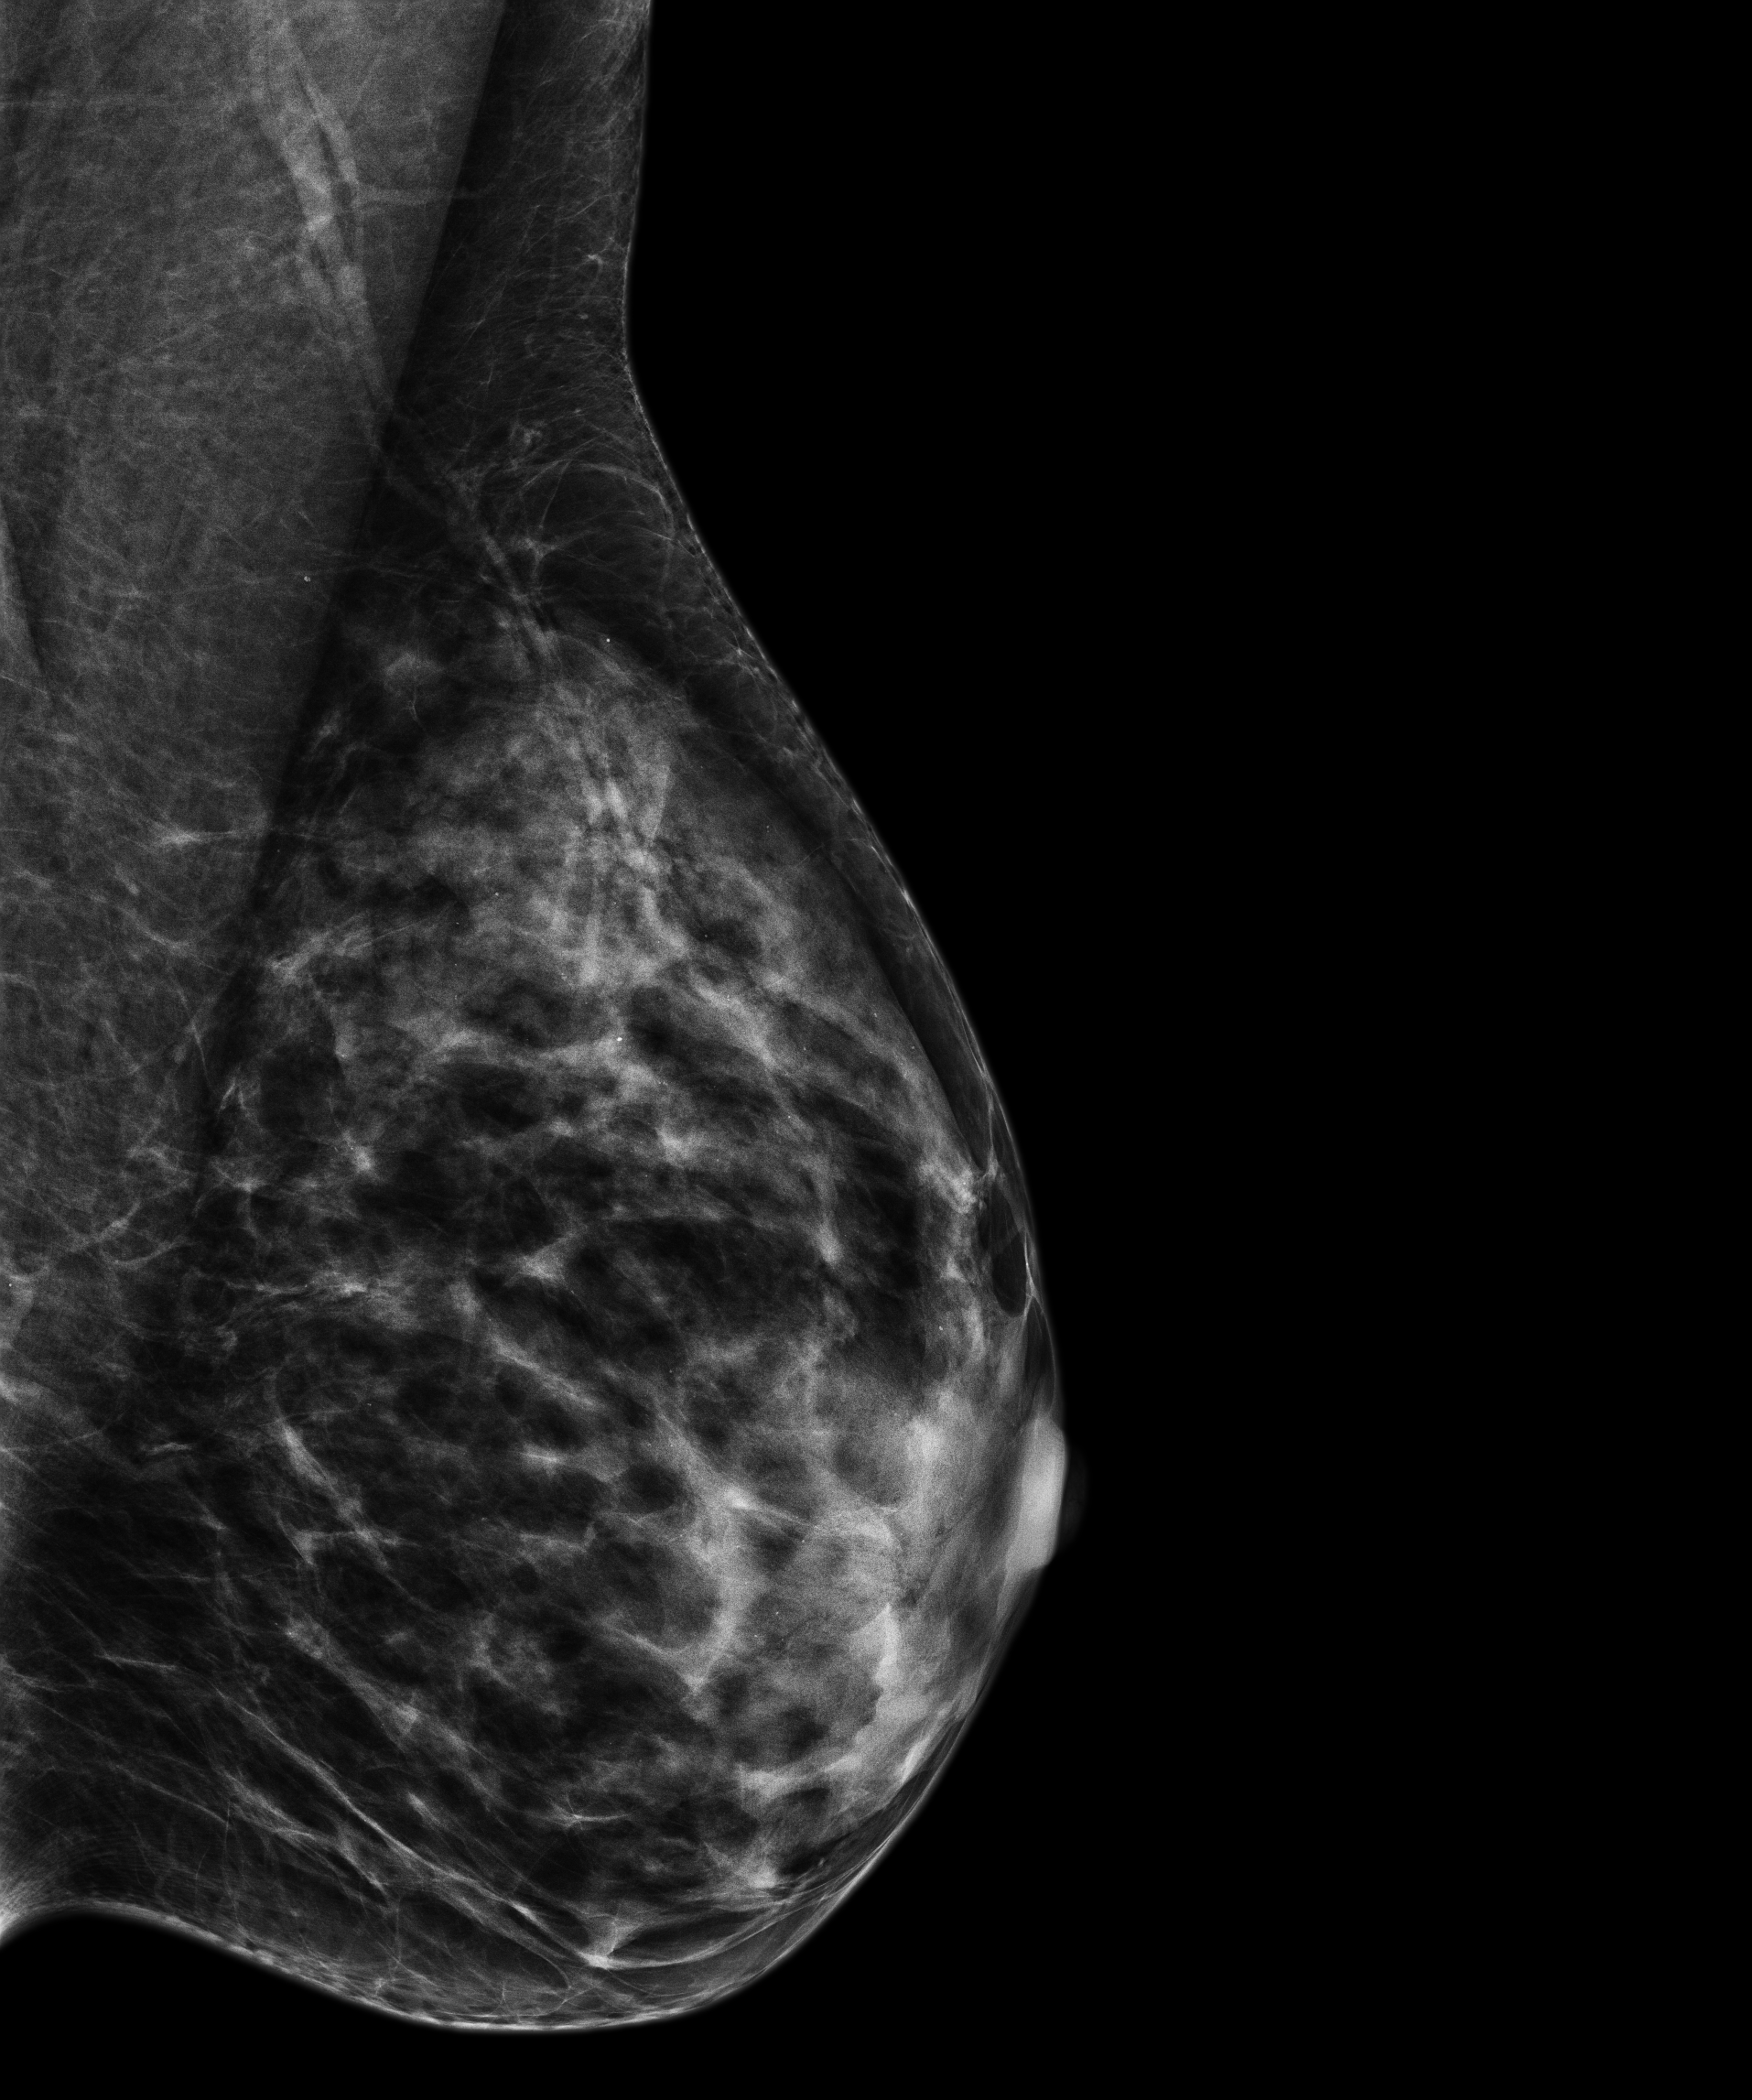
Diagnostic examination (additional views). Patient: female, 47 years.
Image type: full-field digital mammogram. Breast: left. Projection: MLO view.